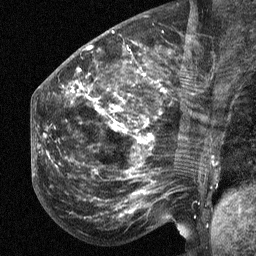
Breast MRI (dynamic contrast-enhanced), one sagittal slice; dynamic contrast-enhanced study with each time point stored as its own series, time point 2 of 3 at this slice position (early post-contrast, ordered by acquisition time); 1.5 T; TE 4.8 ms, TR 27 ms; 256 × 256 image matrix, field of view 200 × 200 mm. Patient: female, 50 years. Case-level facts recorded for this patient, not image findings: setting: breast cancer imaged before/during neoadjuvant chemotherapy; receptor status: HER2-positive.
Outlined on this slice (semi-automatically segmented with operator editing):
- analysis volume of interest (the breast-tissue region the enhancement analysis was run in; not a lesion): bounding box [x1, y1, x2, y2] px = [53, 64, 211, 218]
- tumour enhancement mask (voxels above the 90 % enhancement threshold inside the analysis volume of interest): [72, 90, 164, 194]